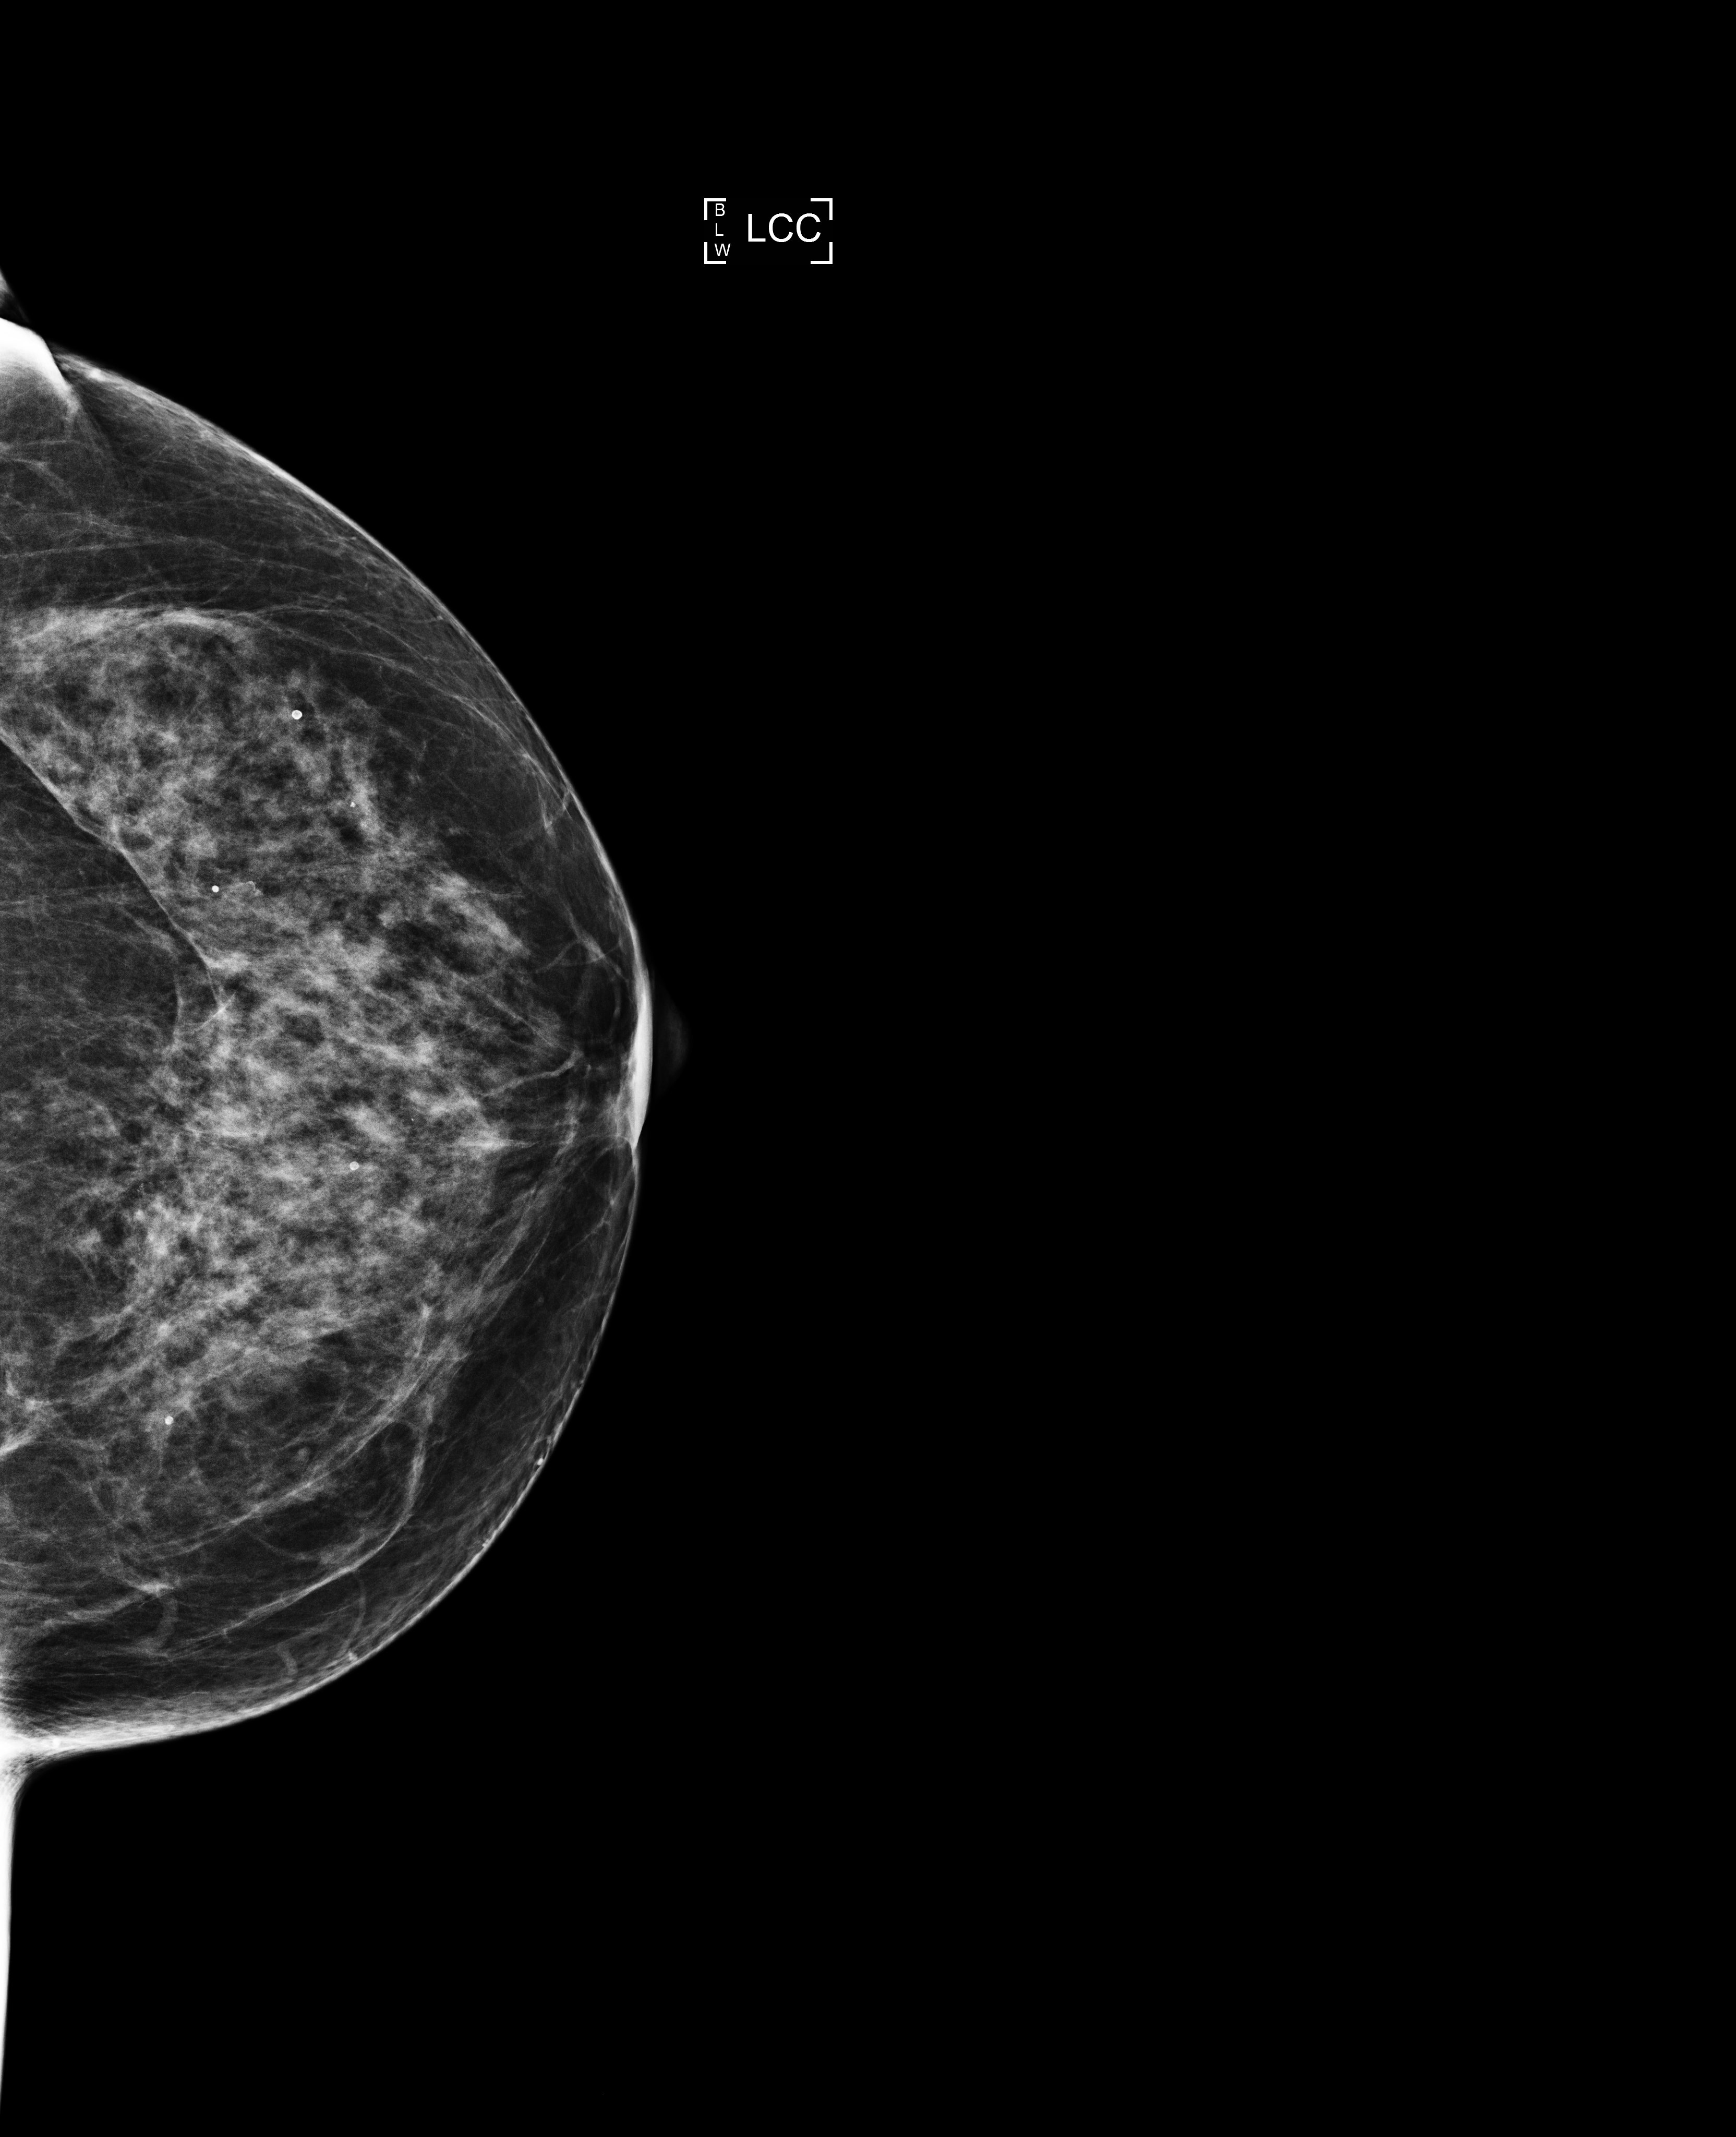
Annual screening mammography examination. Female patient, age 60 years.
Image type: full-field digital mammogram. Breast: left. Projection: craniocaudal (CC) view. Breast density at the screening exam (both breasts): heterogeneously dense (BI-RADS density category c). Final BI-RADS assessment for this screening round (tomosynthesis exam, both breasts): category 2. Recall: no recall after this screen.